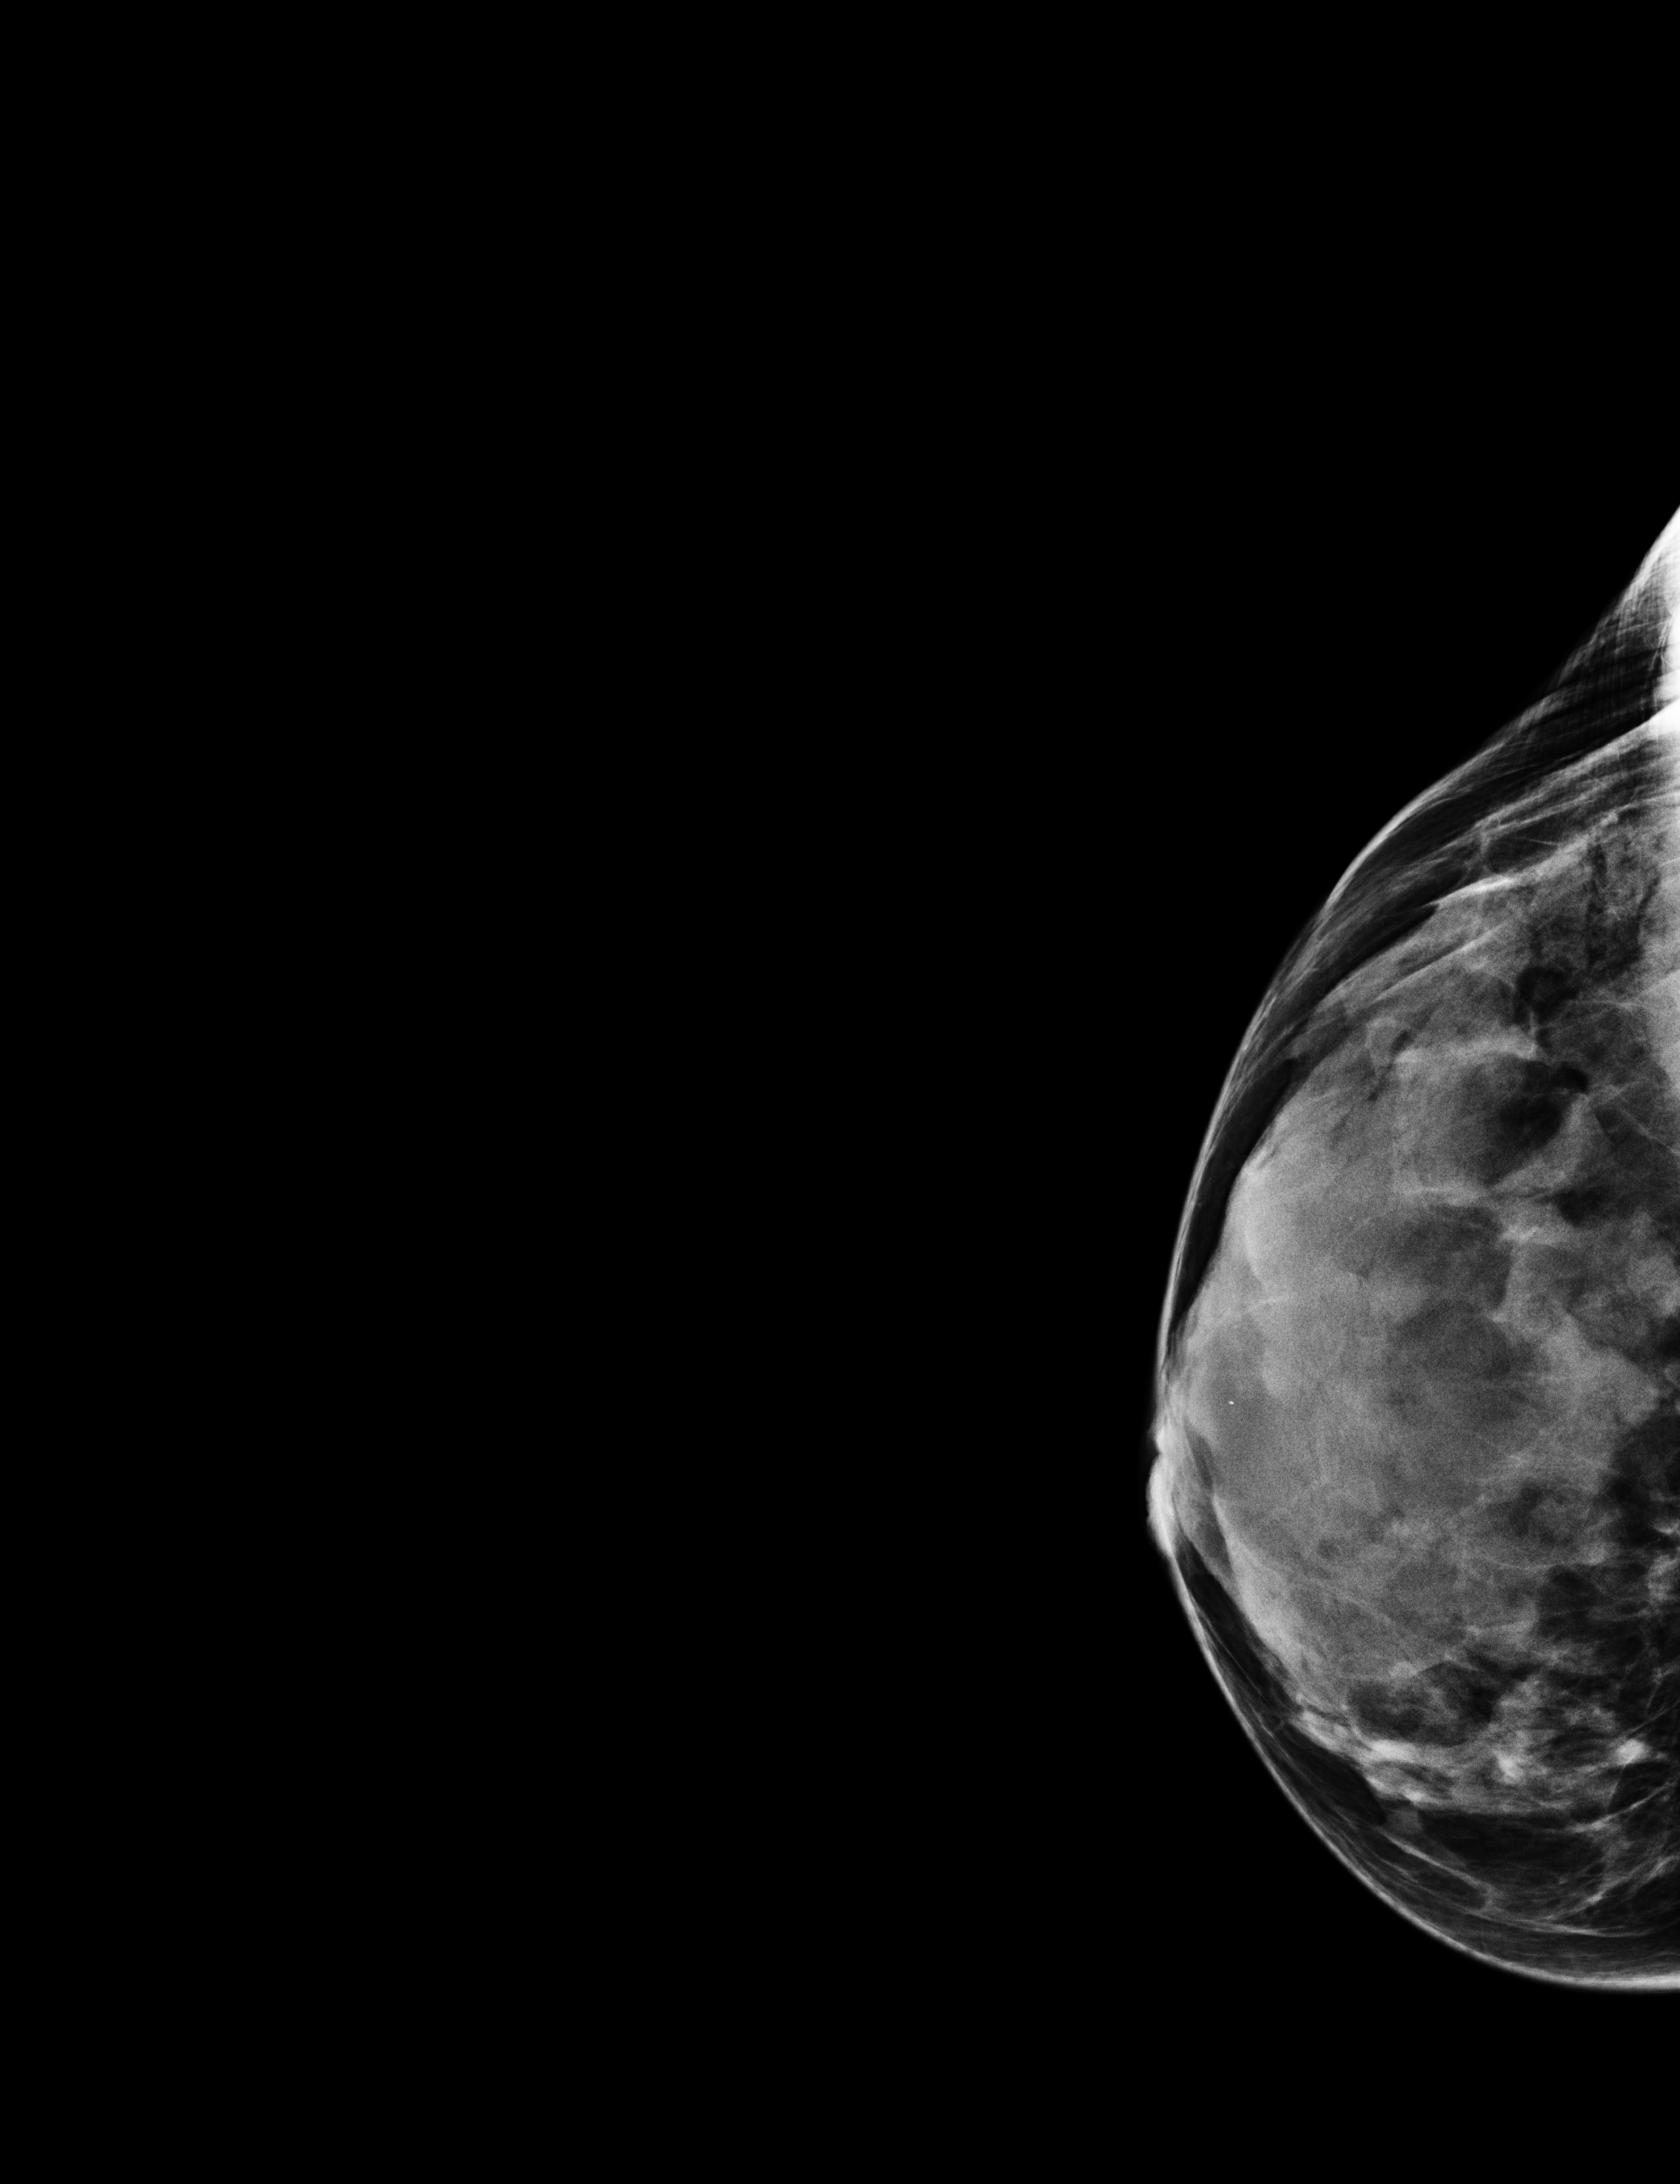
Annual screening mammography examination; system: Selenia Dimensions. Patient aged 59 years (female).
Image type: full-field digital mammogram. Breast: right. Projection: exaggerated CC view (lateral).